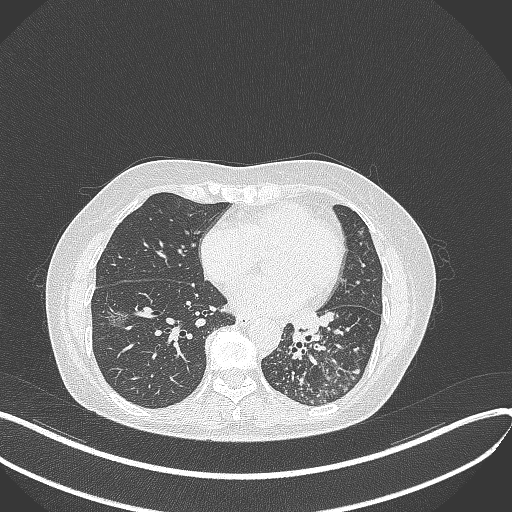
Chest CT, one axial slice. Slice 161 of 429 in the series (ordered by position). Reconstruction kernel B70f. Lung window (W 1500 / L -600 HU). 1 mm slice thickness. 512 × 512 image matrix, field of view 400 × 400 mm. Patient: female, 63 years. From the clinical record (not read from this slice): clinical TNM (as recorded): T1b N0 M0; histopathological grade: G2-3.
Structures marked on this image (bounding box drawn by a radiologist):
- lung tumour (recorded histology: adenocarcinoma): bounding box [x1, y1, x2, y2] px = [285, 307, 325, 347]